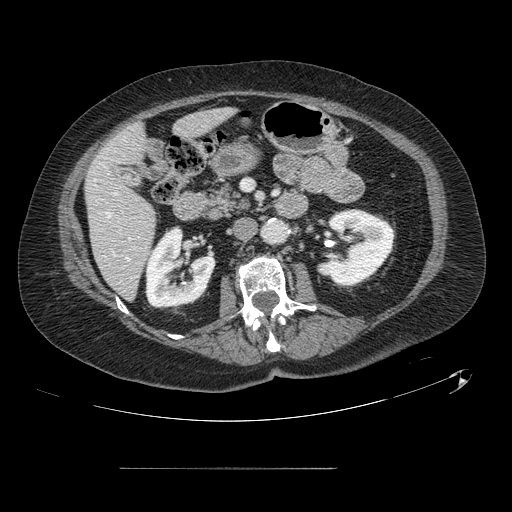
Contrast-enhanced abdominal CT, one axial slice. Position 44 of 148 along the scan axis. Intravenous contrast given. Soft-tissue window (W 400 / L 40 HU). 2.5 mm slice thickness. 512 × 512 image matrix. Female patient, age 75 years. From the clinical record (not read from this slice): diagnosis: colorectal cancer liver metastases, imaged before liver resection; multiple liver metastases: no; largest metastasis: 2.4 cm.
Structures marked on this image (expert manual segmentation):
- hepatic veins: bounding box <107,213,130,260> (left, top, right, bottom; pixels)
- liver: <85,110,231,298>
- planned liver remnant (the part of the liver to remain after resection): <85,110,231,299>